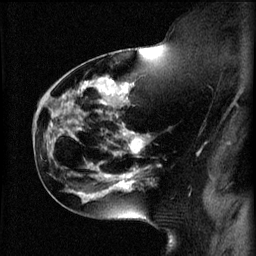
Breast MRI (dynamic contrast-enhanced), one sagittal slice; 3 images stored at this slice position (order not interpretable as contrast timing); 1.5 T; TE 4.2 ms, TR 11 ms; 2 mm slice thickness; 256 × 256 image matrix. Patient: female, 44 years.
Annotated regions visible in this slice (semi-automatically segmented with operator editing):
- analysis volume of interest (the breast-tissue region the enhancement analysis was run in; not a lesion): bounding box [x1, y1, x2, y2] px = [110, 124, 161, 179]
- tumour enhancement mask (voxels above the 70 % enhancement threshold inside the analysis volume of interest): [116, 128, 151, 179]